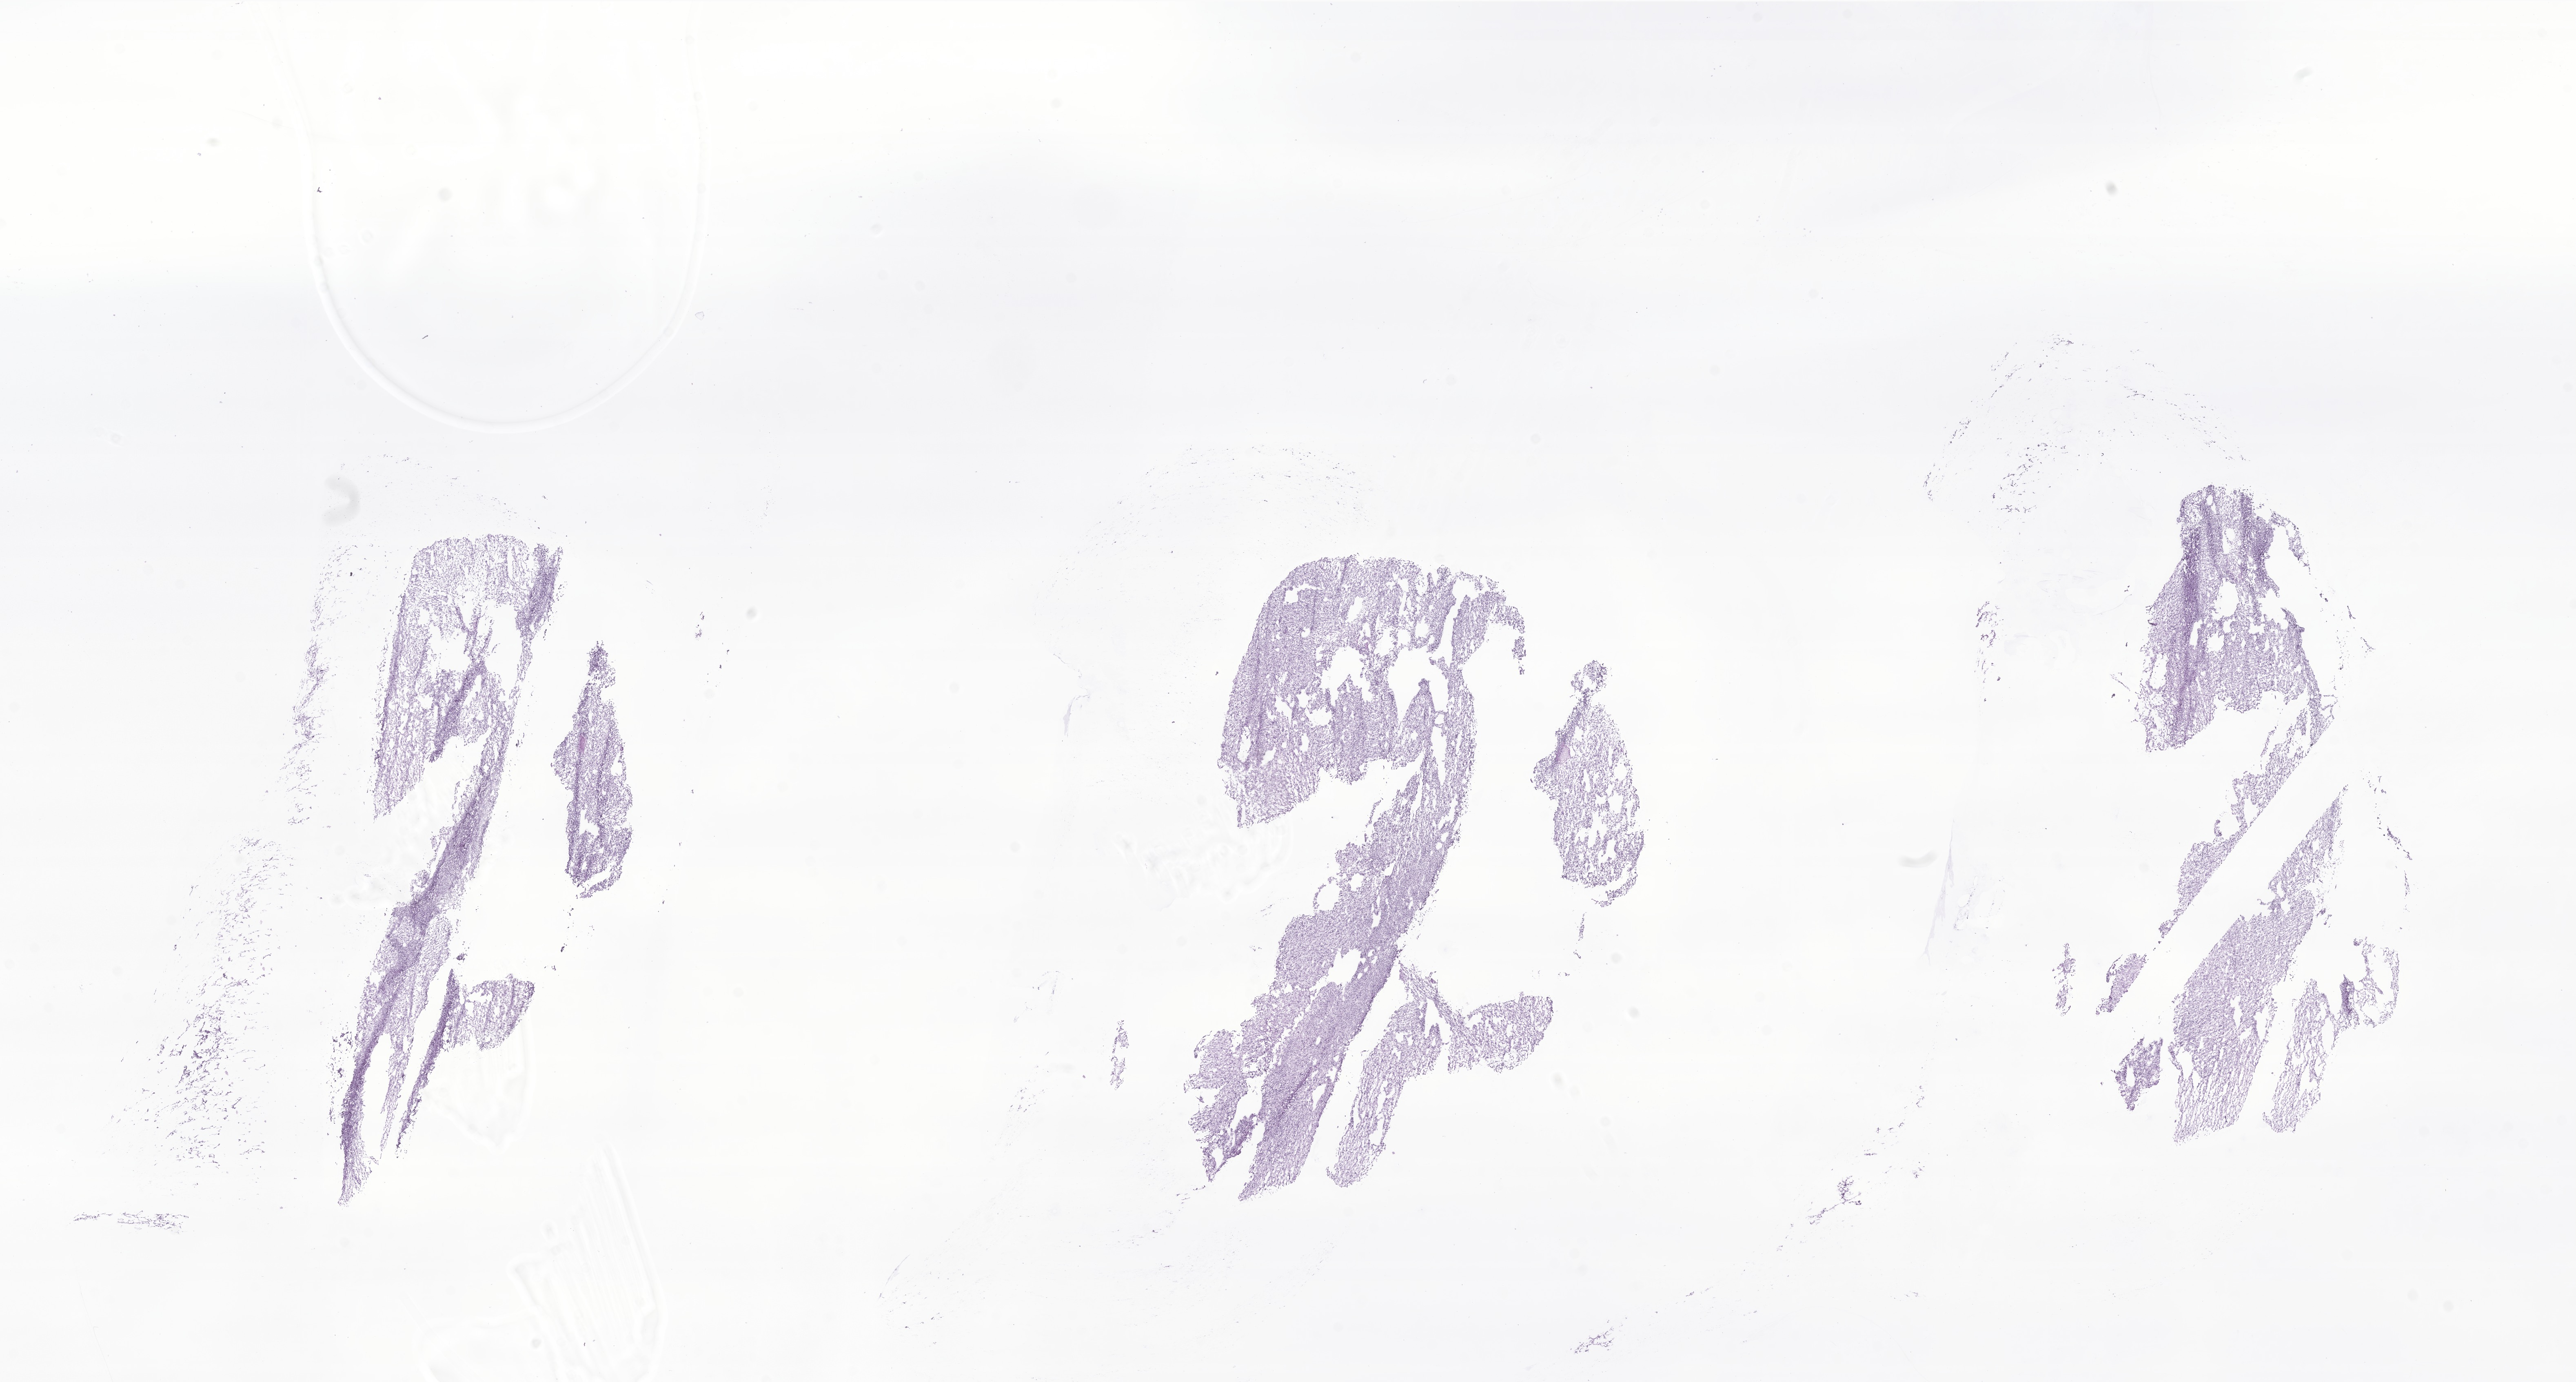
Hematoxylin and eosin (H&E) whole-slide image of tumor tissue from the occipital lobe, a low-resolution overview of the entire scanned area, about 26.6 x 14.3 mm; frozen section (OCT-embedded). Patient: male, age 100 months.
Recorded diagnosis: Neoplasm, uncertain whether benign or malignant.